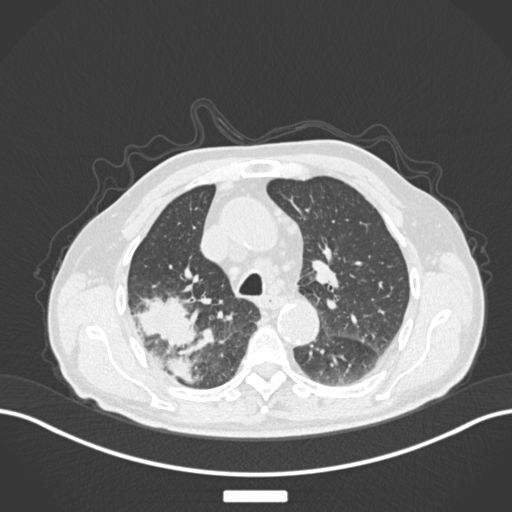
Chest CT, one axial slice; reconstruction kernel B30f; 120 kVp; lung window (W 1500 / L -600 HU); 1 mm slice thickness; 512 × 512 image matrix. Patient: male, 72 years. Case-level facts recorded for this patient, not image findings: clinical TNM (as recorded): T3 N2 M0.
Outlined on this slice (rectangle marked by the reading radiologist):
- lung tumour (recorded histology: adenocarcinoma): bounding box [x1, y1, x2, y2] px = [136, 292, 207, 390]